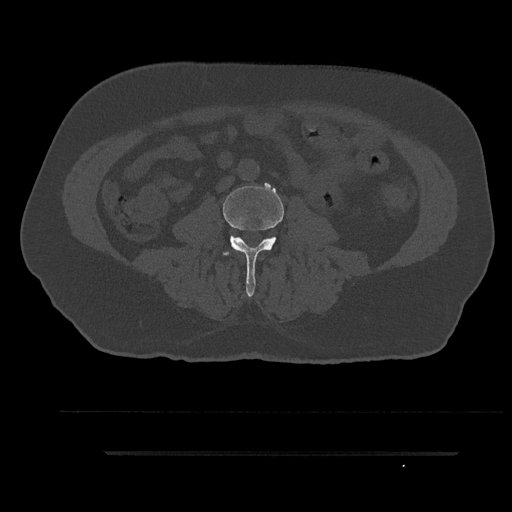
CT including the spine, one axial slice; slice 31 of 797 in the series (ordered by position); reconstruction kernel Br40s/3; 120 kVp; bone window (W 1800 / L 400 HU); 512 × 512 image matrix, field of view 432 × 432 mm. Male patient, age 63 years. From the clinical record (not read from this slice): primary cancer: renal.
Structures marked on this image (semi-automatic segmentation, software-assisted and operator-edited):
- L3 vertebra: box from (x=222, y=185) to (x=284, y=297) px